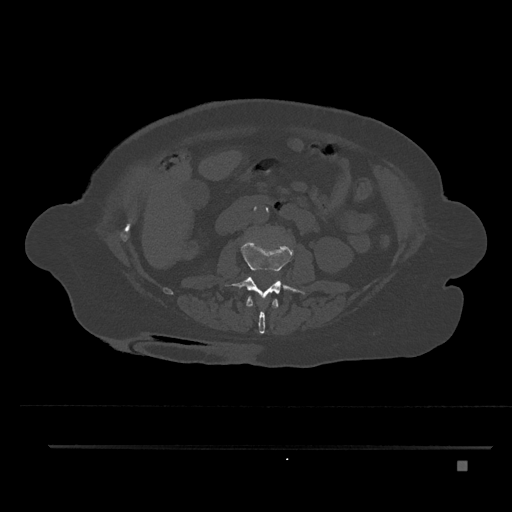
CT including the spine, one axial slice. Slice 174 of 797 in the series (ordered by position). Reconstruction kernel Br40s/3. 120 kVp. Bone window (W 1800 / L 400 HU). 0.5 mm slice thickness. 512 × 512 image matrix, field of view 437 × 437 mm. Female patient, age 76 years. Case-level facts recorded for this patient, not image findings: primary cancer: lung; vertebrae with lytic lesions (as recorded): T11, L3.
Outlined on this slice (semi-automatically segmented with operator editing):
- L1 vertebra: bounding box (x1, y1, x2, y2) in pixels: (246, 296, 279, 334)
- L2 vertebra: (225, 239, 305, 303)